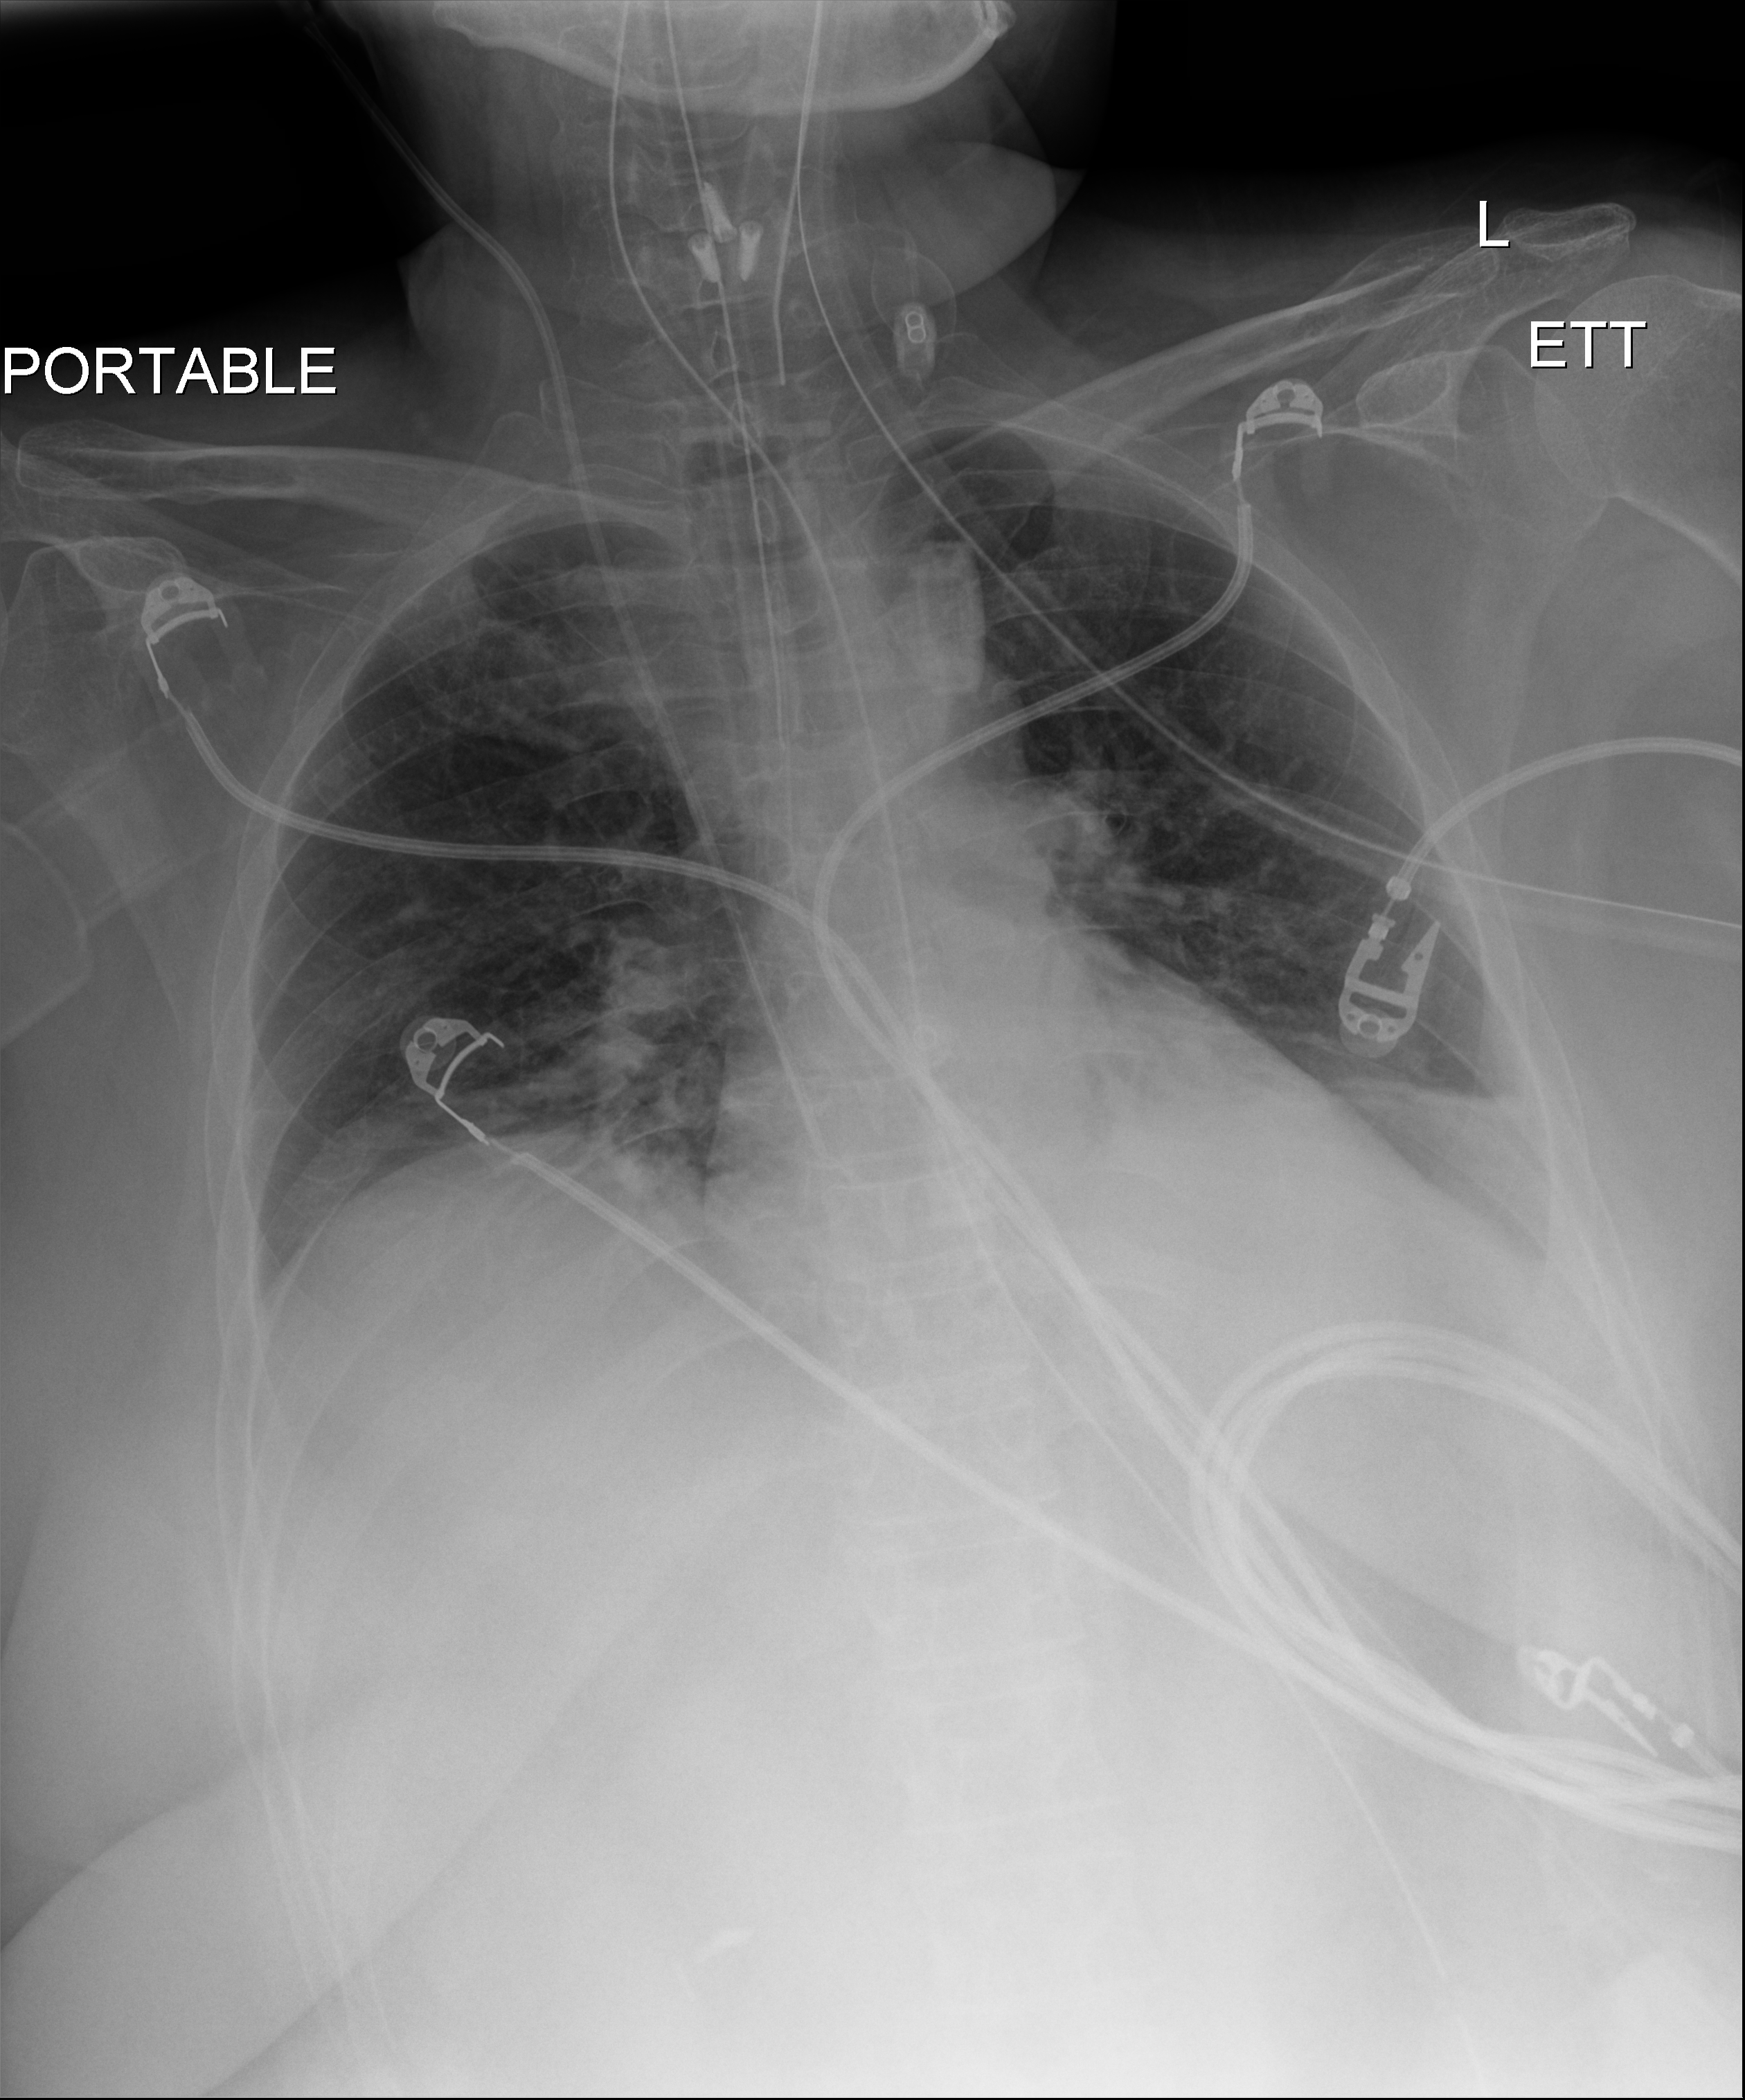
Bedside chest radiograph (digital radiography). Female patient hospitalised with COVID-19, age 18–59 years.
Admission-level facts for this patient (not findings on this image; timing relative to this image not recorded): admitted to intensive care during this hospital stay: yes; mechanically ventilated during this hospital stay: no; length of hospital stay: 44 days.